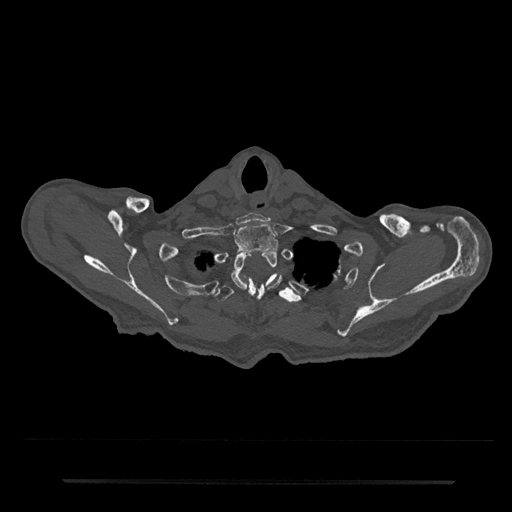
CT including the spine, one axial slice; bone window (W 1800 / L 400 HU); 512 × 512 image matrix, field of view 427 × 427 mm. Male patient, age 74 years. From the clinical record (not read from this slice): primary cancer: prostate.
Outlined on this slice (semi-automatically segmented with operator editing):
- T1 vertebra: bounding box [x1, y1, x2, y2] px = [234, 223, 280, 253]
- T2 vertebra: [231, 249, 282, 300]
- T3 vertebra: [214, 274, 301, 303]